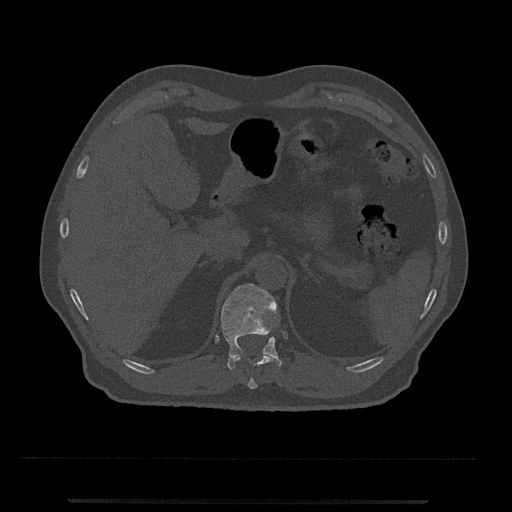
CT including the spine, one axial slice. Position 429 of 797 along the scan axis. Reconstruction kernel Br40s/3. Bone window (W 1800 / L 400 HU). 512 × 512 image matrix, field of view 419 × 419 mm. Male patient, age 63 years. From the clinical record (not read from this slice): primary cancer: prostate.
Outlined on this slice (semi-automatically segmented with operator editing):
- T11 vertebra: bounding box <234,353,274,389> (left, top, right, bottom; pixels)
- T12 vertebra: <221,283,282,370>